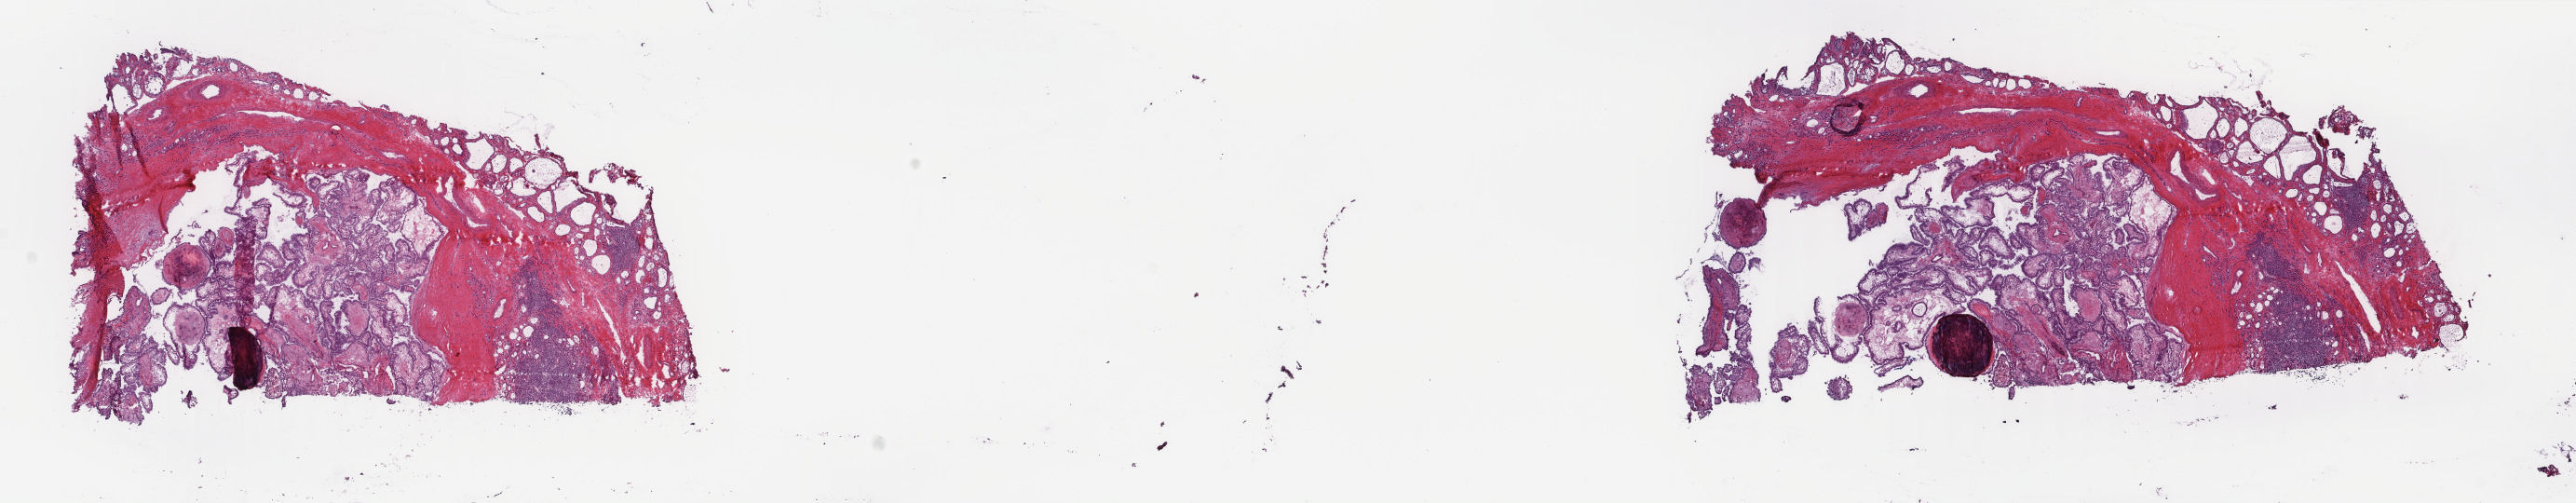
H&E-stained whole-slide image — shown as a low-resolution overview of the whole scanned area (about 22.0 x 4.3 mm), frozen section from the top of the tissue portion, primary tumour sample from the thyroid. Female, age 50 years at initial diagnosis. Pathologist review of this section (percent, as recorded): tumour cells 50%, tumour nuclei 75%, normal cells 25%, stromal cells 25%, necrosis 0%. Infiltration values recorded for this section: lymphocyte infiltration 10%, monocyte infiltration 1%, neutrophil infiltration 0%.
Lymph nodes positive (case pathology): 12 of 56 examined. AJCC pathologic stage: IVA (7th edition). Histologic diagnosis: Papillary adenocarcinoma, NOS (thyroid gland). TNM: T2 N1b M0. Laterality: bilateral.